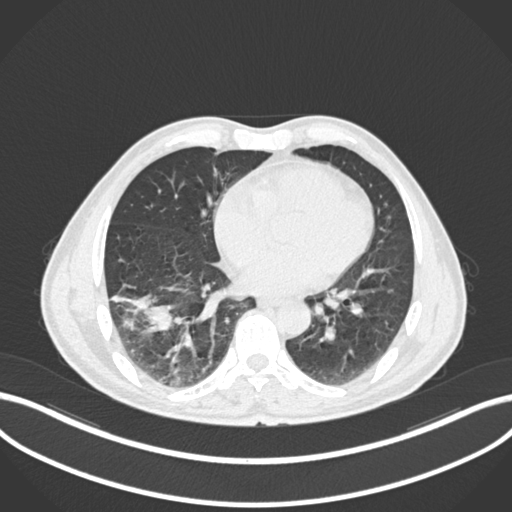
Chest CT, one axial slice. Slice 66 of 208 in the series (ordered by position). Lung window (W 1500 / L -600 HU). 1 mm slice thickness. 512 × 512 image matrix, field of view 400 × 400 mm. Male patient, age 58 years. From the clinical record (not read from this slice): clinical TNM (as recorded): T3 N0 M0.
Structures marked on this image (bounding box drawn by a radiologist):
- lung tumour (recorded histology: squamous cell carcinoma): bounding box [x1, y1, x2, y2] px = [109, 281, 177, 335]